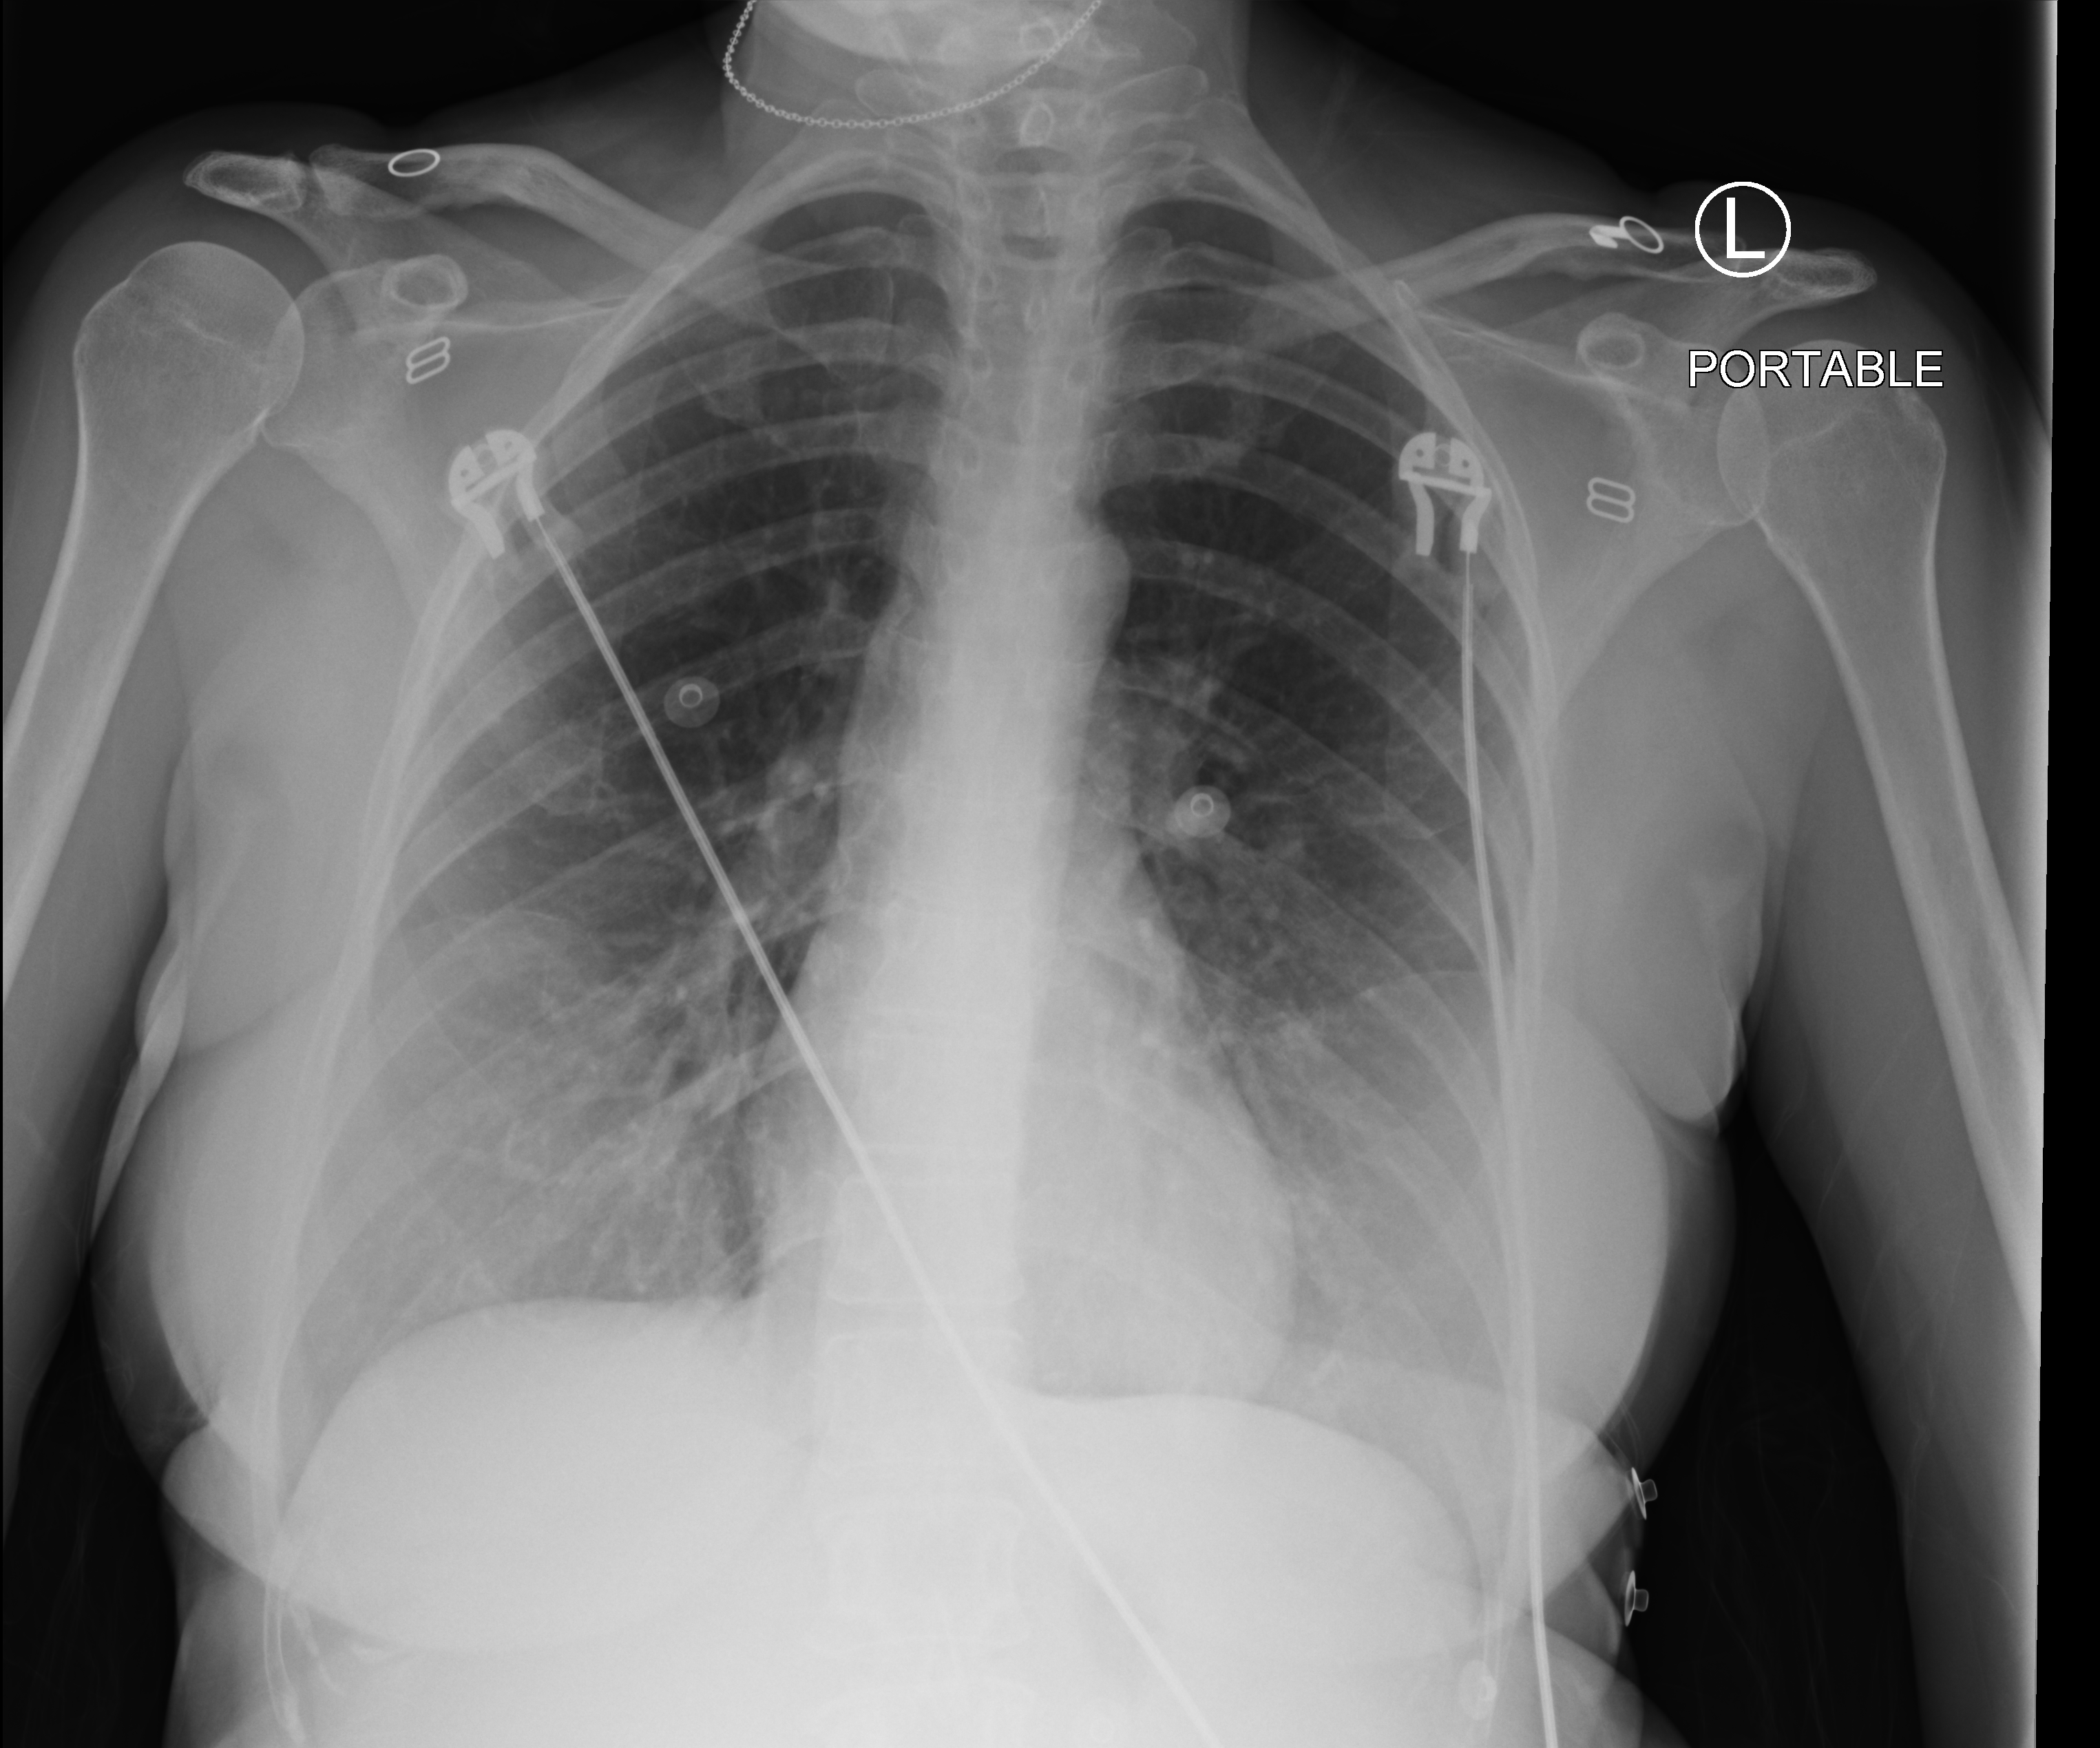
Portable chest radiograph, anteroposterior (AP) projection. Female patient hospitalised with COVID-19, age 18–59 years.
Admission-level facts for this patient (not findings on this image; timing relative to this image not recorded): admitted to intensive care during this hospital stay: no.